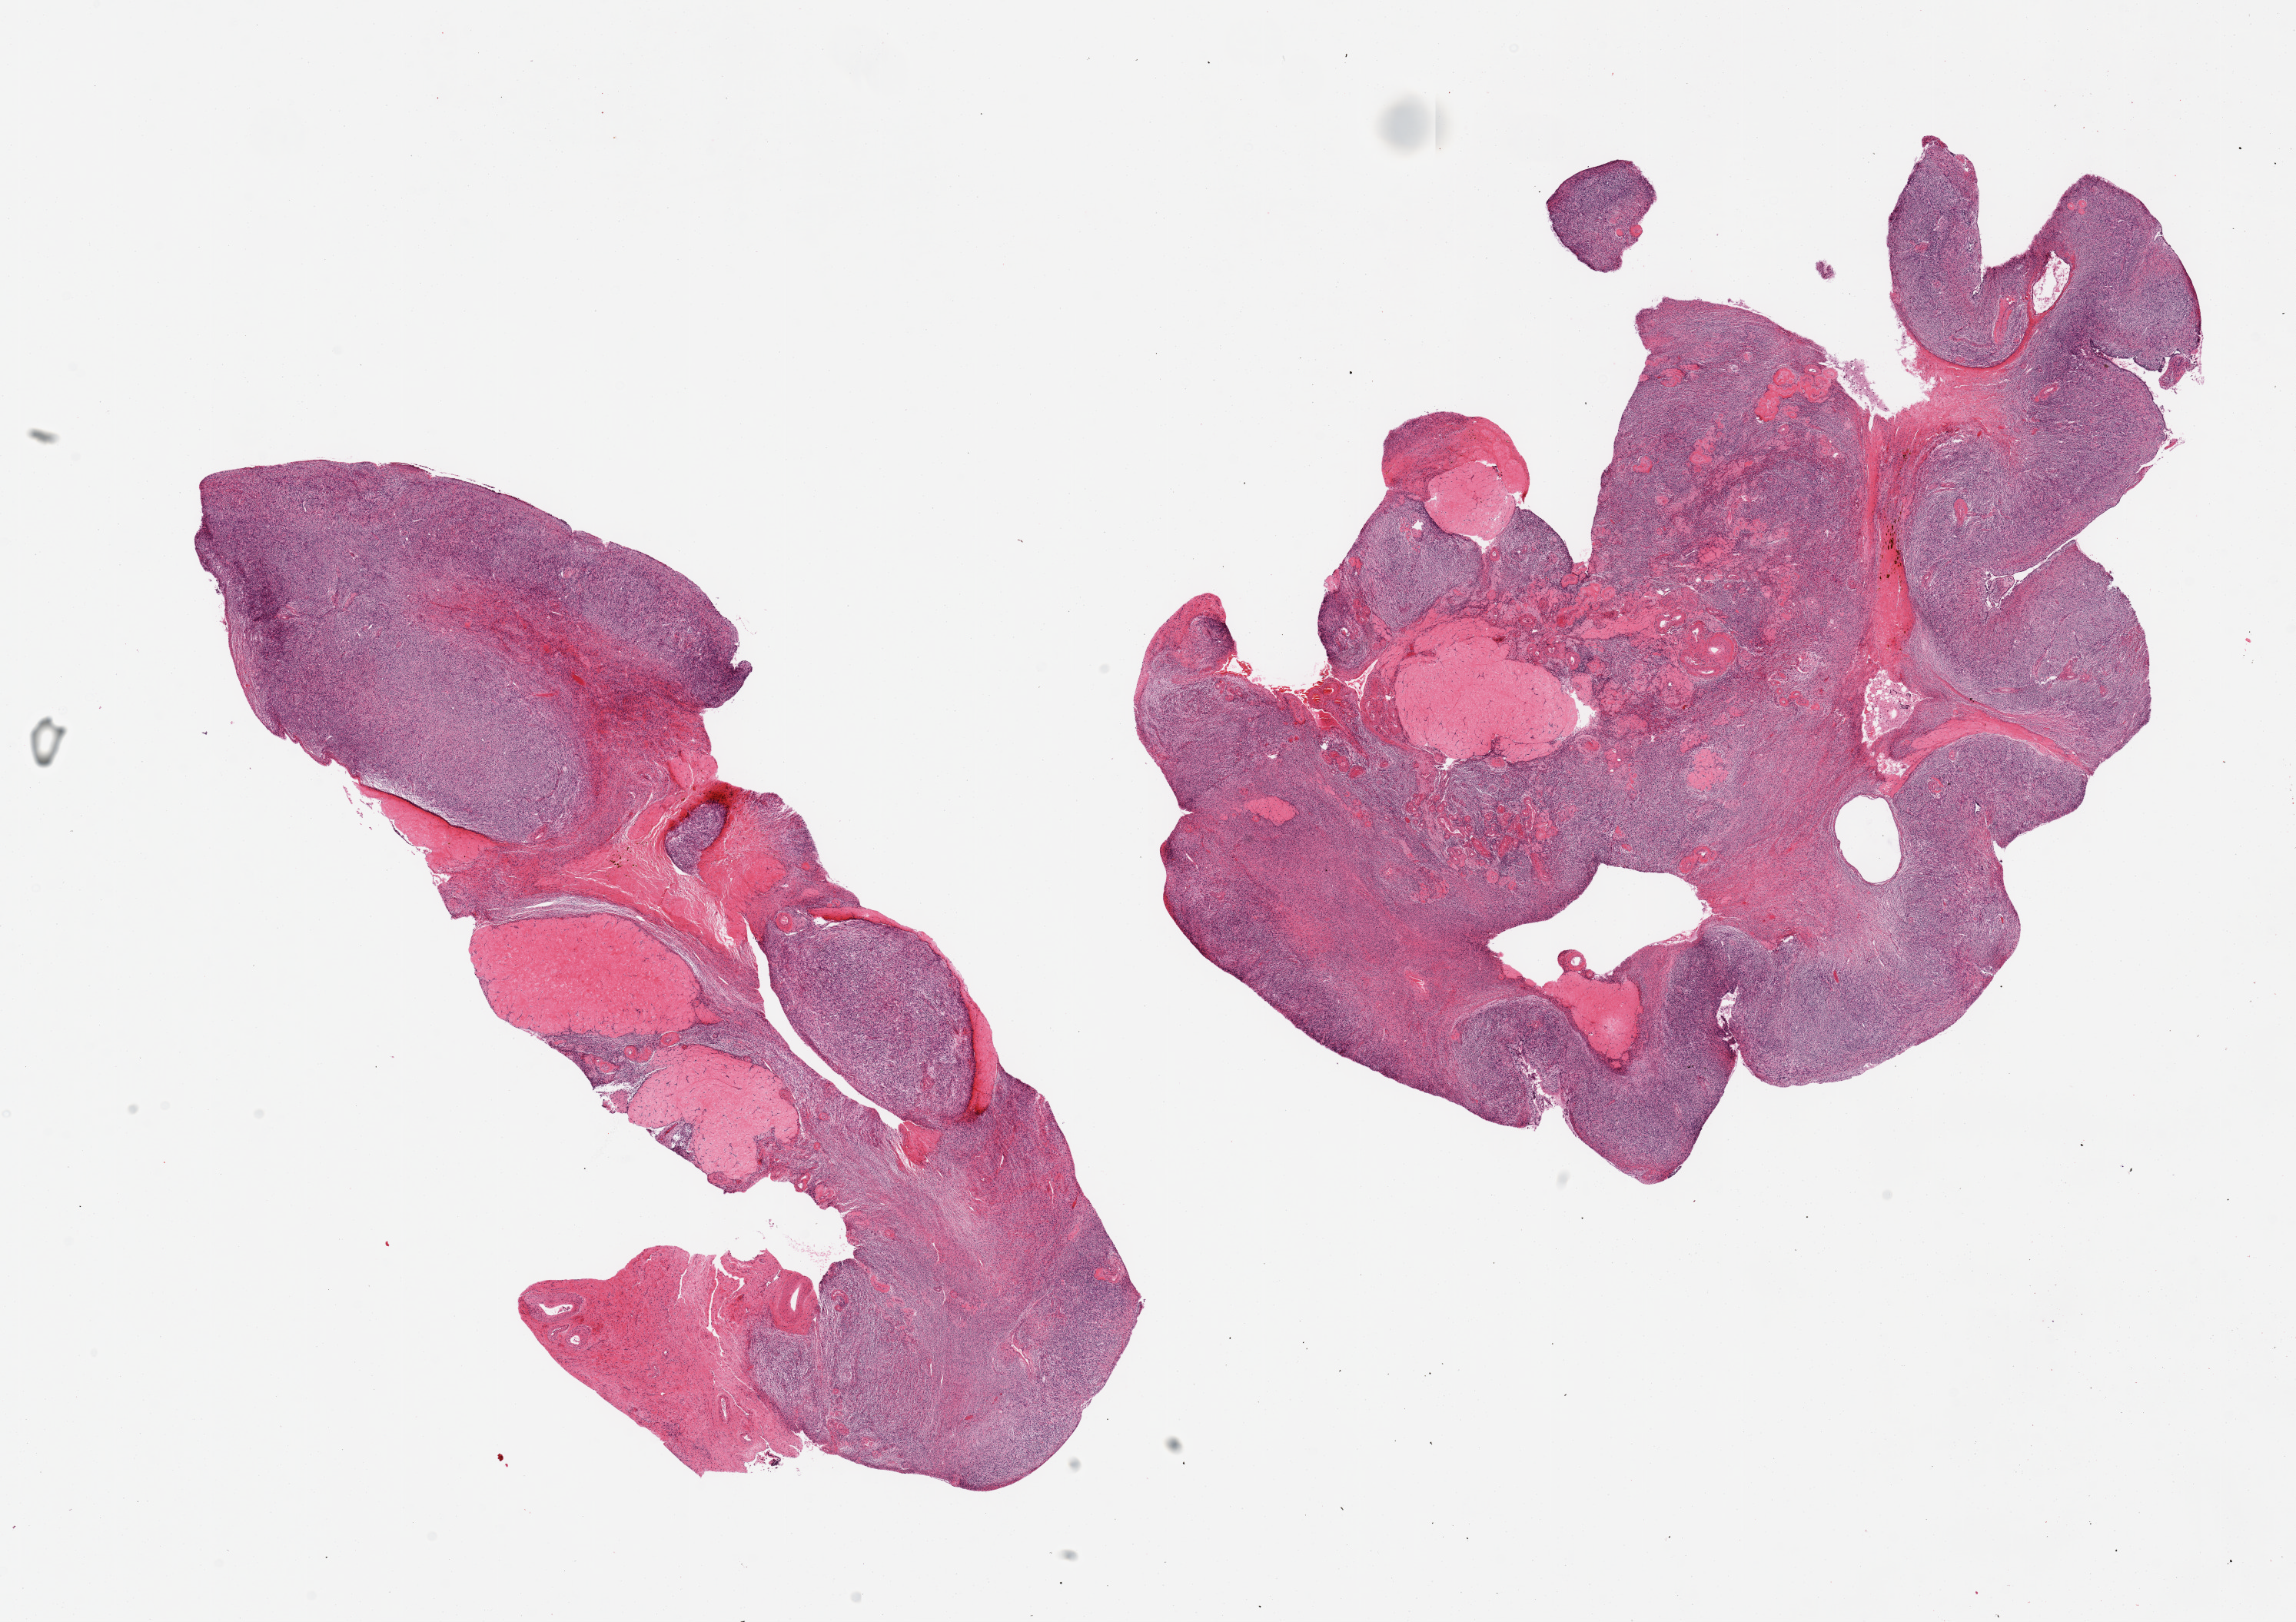
Digitized hematoxylin and eosin (H&E)-stained section, brightfield, low-resolution overview of the scanned area, about 23.6 x 16.7 mm (from a 20x scan); PAXgene-fixed paraffin-embedded (PFPE) section; section of ovary (target tissue); donor tissue sample. Donor: female.
- reviewer comment on this tissue sample: 2 pieces, multiple corpora albicantia